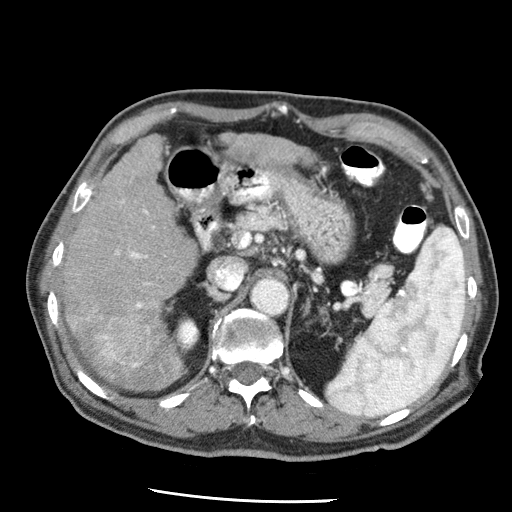
Contrast-enhanced abdominal CT (liver protocol), one axial slice; slice 28 of 79 in the series (ordered by position); reconstruction kernel STANDARD; 120 kVp; soft-tissue window (W 400 / L 40 HU); 2.5 mm slice thickness; 512 × 512 image matrix, field of view 320 × 320 mm. From the clinical record (not read from this slice): diagnosis: hepatocellular carcinoma (patient treated with transarterial chemoembolisation; whether this scan precedes or follows treatment is not stated here); TNM stage (as recorded): Stage-IIIA; Child-Pugh class: A; tumour nodularity: multinodular; tumour size: 7 cm.
Structures marked on this image (semi-automatic segmentation, software-assisted and operator-edited):
- liver parenchyma outside the tumour (the mass and vessels are separate outlines, so this box may not span the whole liver): bounding box (x1, y1, x2, y2) in pixels: (58, 135, 198, 388)
- mass: (94, 310, 159, 371)
- liver vessels: (87, 200, 154, 368)